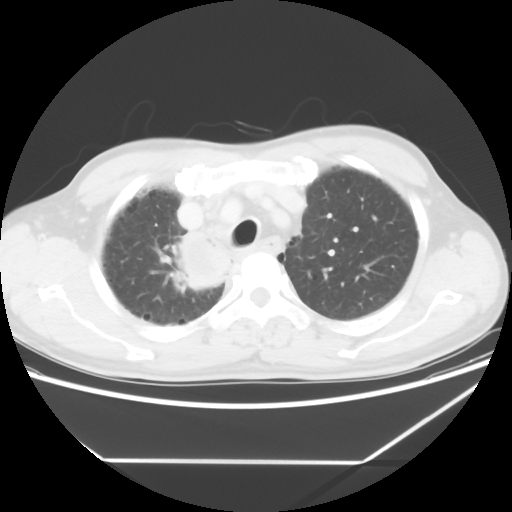
Chest CT, one axial slice; position 48 of 60 along the scan axis; lung window (W 1500 / L -600 HU); 5 mm slice thickness; 512 × 512 image matrix, field of view 367 × 367 mm. Male patient, age 58 years. From the clinical record (not read from this slice): clinical TNM (as recorded): T2 N2 M0.
Structures marked on this image (bounding box drawn by a radiologist):
- lung tumour (recorded histology: squamous cell carcinoma): bounding box <171,230,239,291> (left, top, right, bottom; pixels)